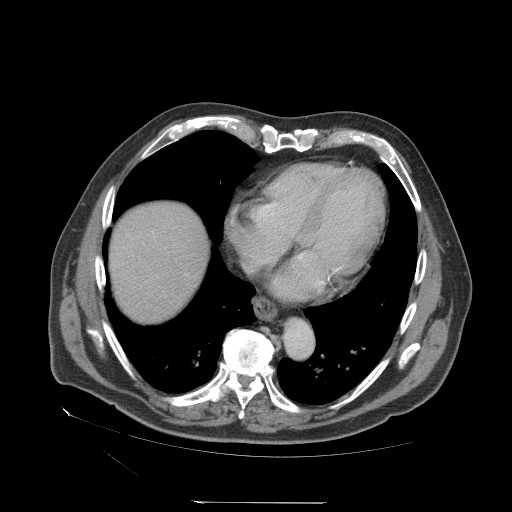
Contrast-enhanced abdominal CT (liver protocol), one axial slice; slice 69 of 83 in the series (ordered by position); reconstruction kernel STANDARD; soft-tissue window (W 400 / L 40 HU); 512 × 512 image matrix, field of view 460 × 460 mm. Case-level facts recorded for this patient, not image findings: diagnosis: hepatocellular carcinoma (patient treated with transarterial chemoembolisation; whether this scan precedes or follows treatment is not stated here); TNM stage (as recorded): Stage-I; Child-Pugh class: A.
Annotated regions visible in this slice (semi-automatically segmented with operator editing):
- liver parenchyma outside the tumour (the mass and vessels are separate outlines, so this box may not span the whole liver): bounding box (x1, y1, x2, y2) in pixels: (108, 202, 208, 322)